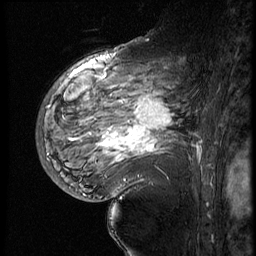
Breast MRI (dynamic contrast-enhanced), one sagittal slice. Position 39 of 60 along the scan axis. 4 images stored at this slice position (order not interpretable as contrast timing). 1.5 T. TE 4.2 ms, TR 9 ms. 2.5 mm slice thickness. 256 × 256 image matrix, field of view 180 × 180 mm. Female patient, age 56 years. Case-level facts recorded for this patient, not image findings: setting: breast cancer imaged before/during neoadjuvant chemotherapy; receptor status: HER2-positive.
Outlined on this slice (semi-automatically segmented with operator editing):
- analysis volume of interest (the breast-tissue region the enhancement analysis was run in; not a lesion): bounding box (x1, y1, x2, y2) in pixels: (82, 83, 199, 177)
- tumour enhancement mask (voxels above the 140 % enhancement threshold inside the analysis volume of interest): (102, 98, 174, 162)